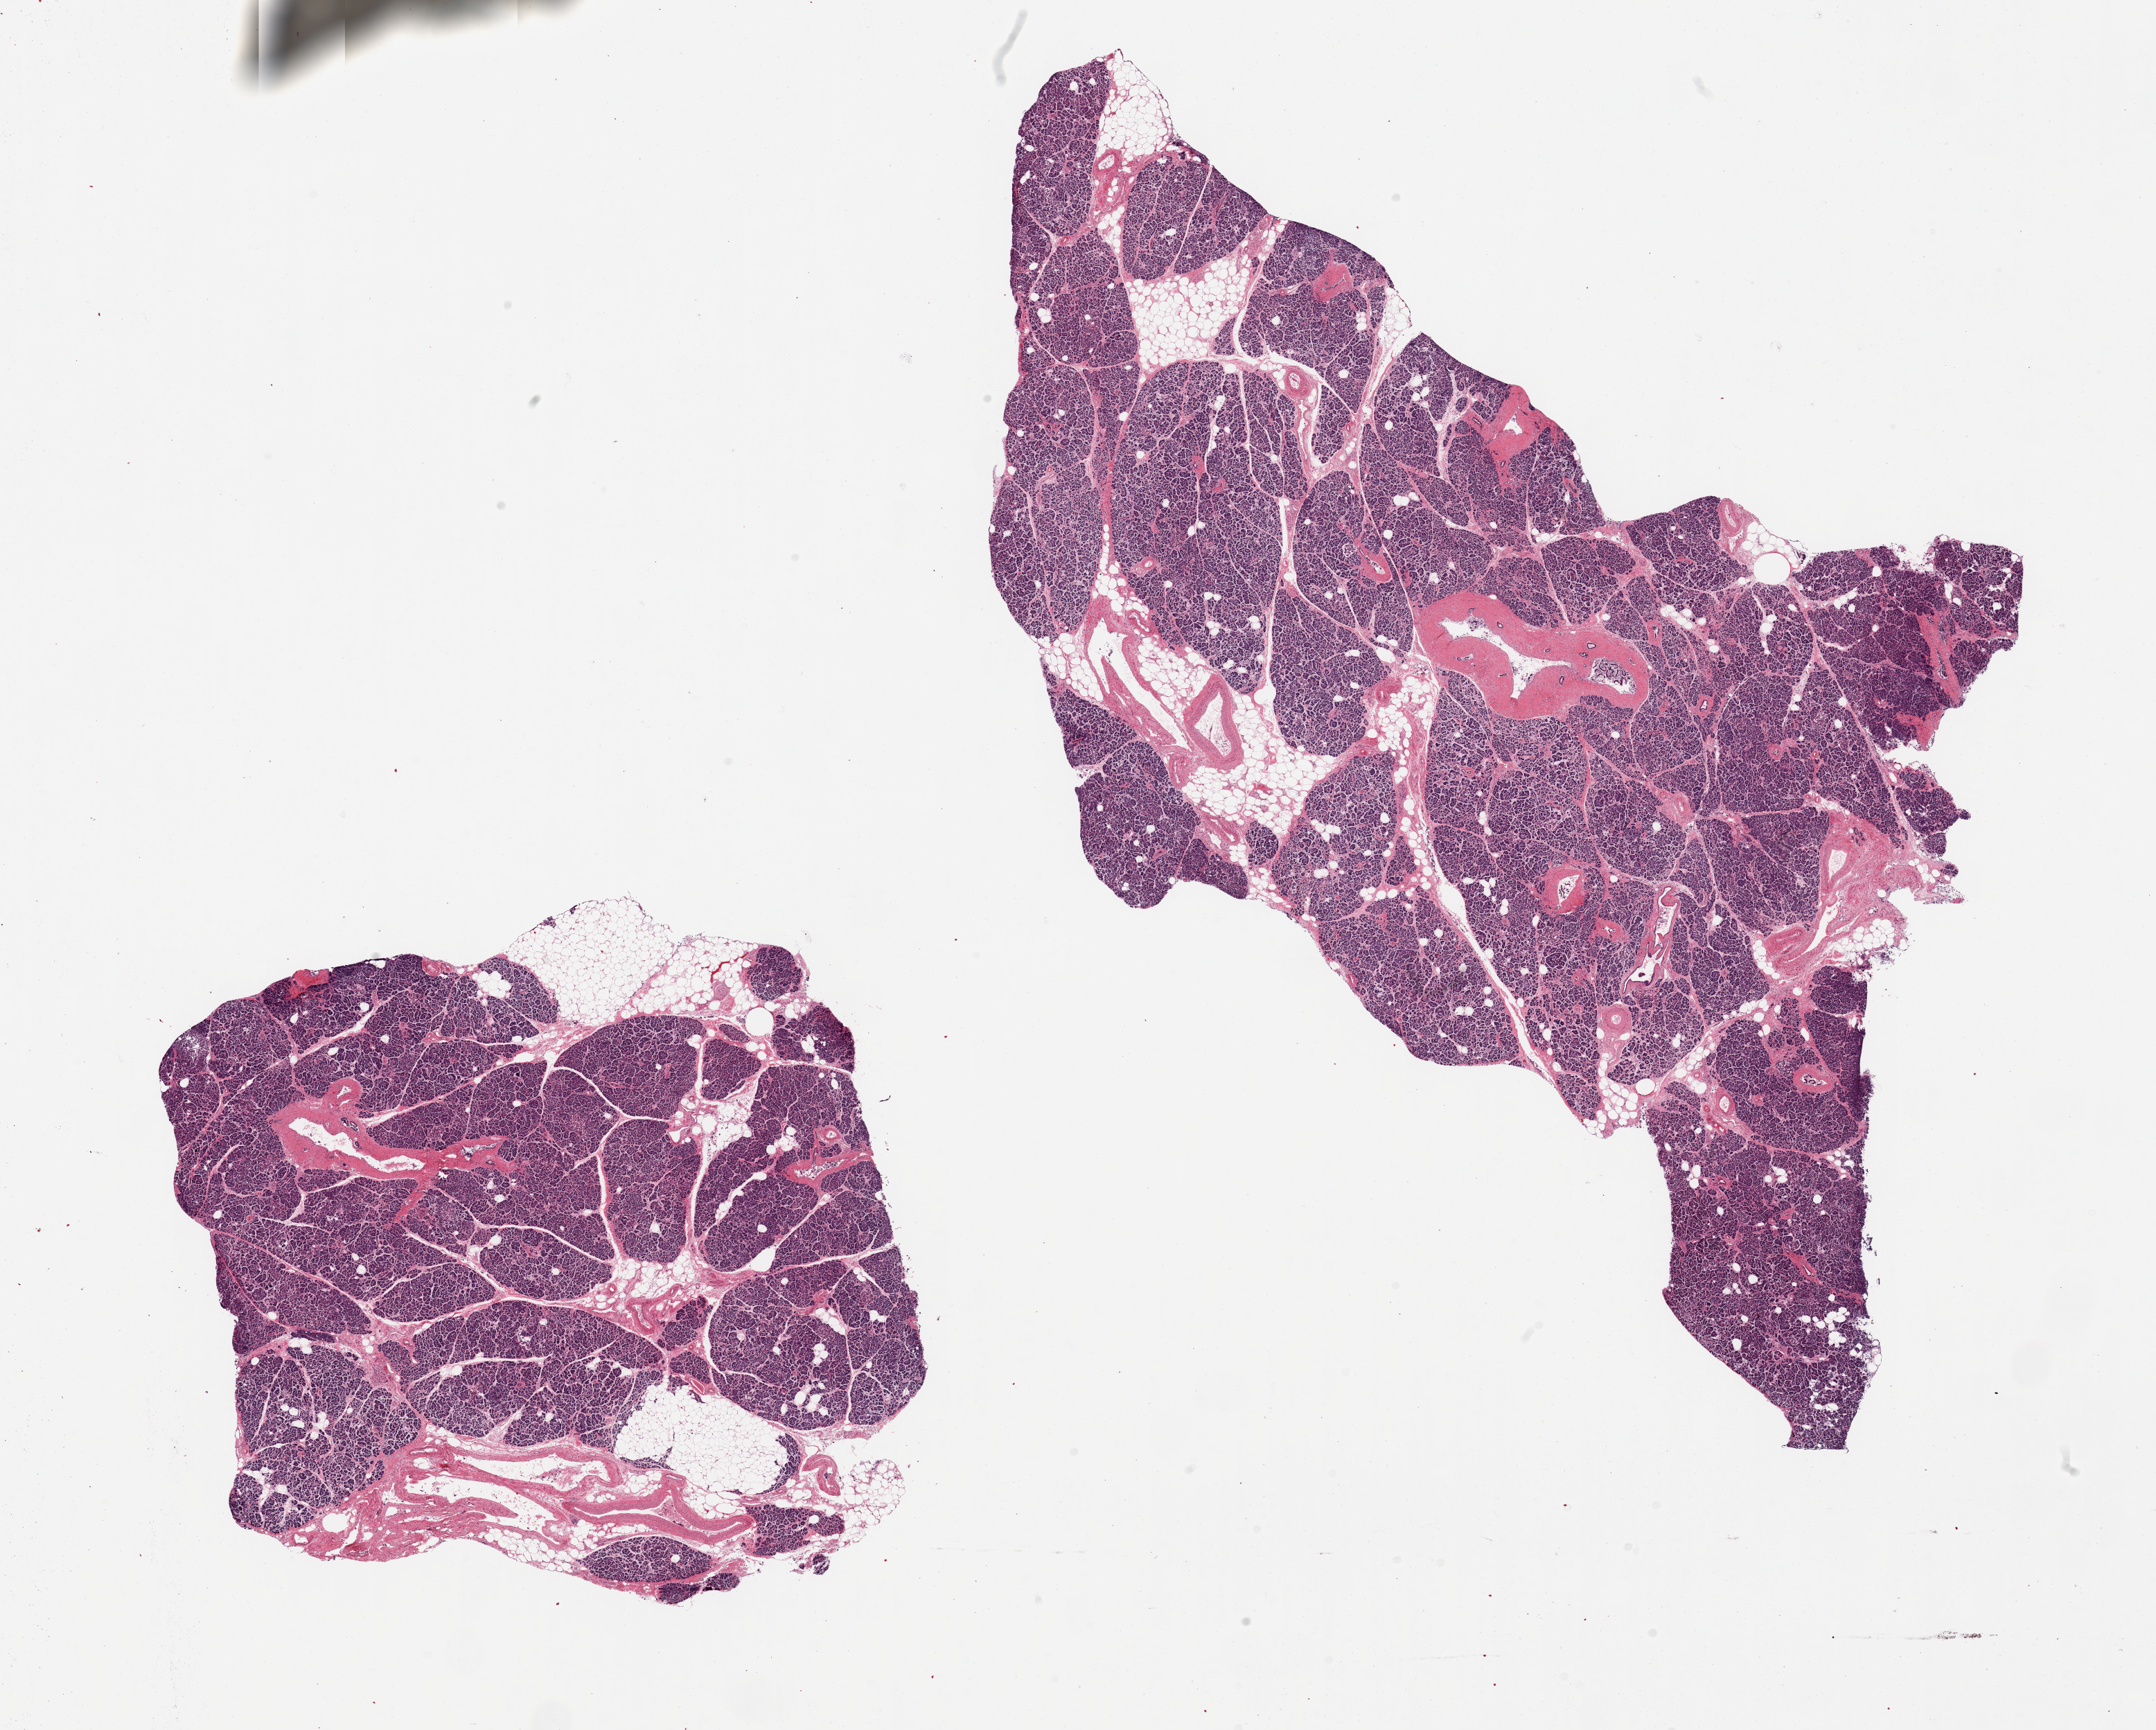
H&E whole-slide image — low-resolution overview of the scanned area, about 24.6 x 19.7 mm; PAXgene-fixed, paraffin-embedded tissue; section of pancreas (target tissue); tissue donor sample. Donor sex: male.
* review note (as recorded): 2 pieces, occasional islets discernable, not well-preserved, moderately advanced saponification